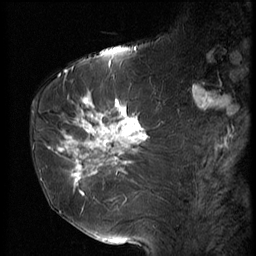
Breast MRI (dynamic contrast-enhanced), one sagittal slice; slice 26 of 56 in the series (ordered by position); 3 images stored at this slice position (order not interpretable as contrast timing); 1.5 T; TE 4.2 ms, TR 9 ms; 2.5 mm slice thickness; 256 × 256 image matrix, field of view 180 × 180 mm. Patient: female, 61 years. Case-level facts recorded for this patient, not image findings: setting: breast cancer imaged before/during neoadjuvant chemotherapy; receptor status: HR-positive, HER2-negative.
Outlined on this slice (semi-automatically segmented with operator editing):
- analysis volume of interest (the breast-tissue region the enhancement analysis was run in; not a lesion): bounding box (x1, y1, x2, y2) in pixels: (47, 89, 153, 191)
- tumour enhancement mask (voxels above the 140 % enhancement threshold inside the analysis volume of interest): (48, 99, 148, 185)